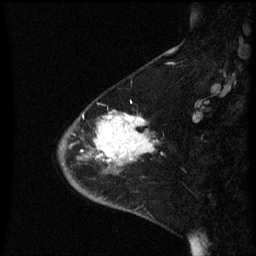
Breast MRI (dynamic contrast-enhanced), one sagittal slice. Slice 19 of 60 in the series (ordered by position). Dynamic contrast-enhanced series, image 2 of 3 at this slice position (ordered by acquisition). 1.5 T. TE 4.2 ms, TR 8.4 ms. 2.3 mm slice thickness. 256 × 256 image matrix. Patient: female, 46 years. From the clinical record (not read from this slice): setting: breast cancer imaged before/during neoadjuvant chemotherapy; receptor status: HER2-positive.
Outlined on this slice (semi-automatic segmentation, software-assisted and operator-edited):
- analysis volume of interest (the breast-tissue region the enhancement analysis was run in; not a lesion): bounding box <59,108,158,187> (left, top, right, bottom; pixels)
- tumour enhancement mask (voxels above the 70 % enhancement threshold inside the analysis volume of interest): <78,110,153,163>